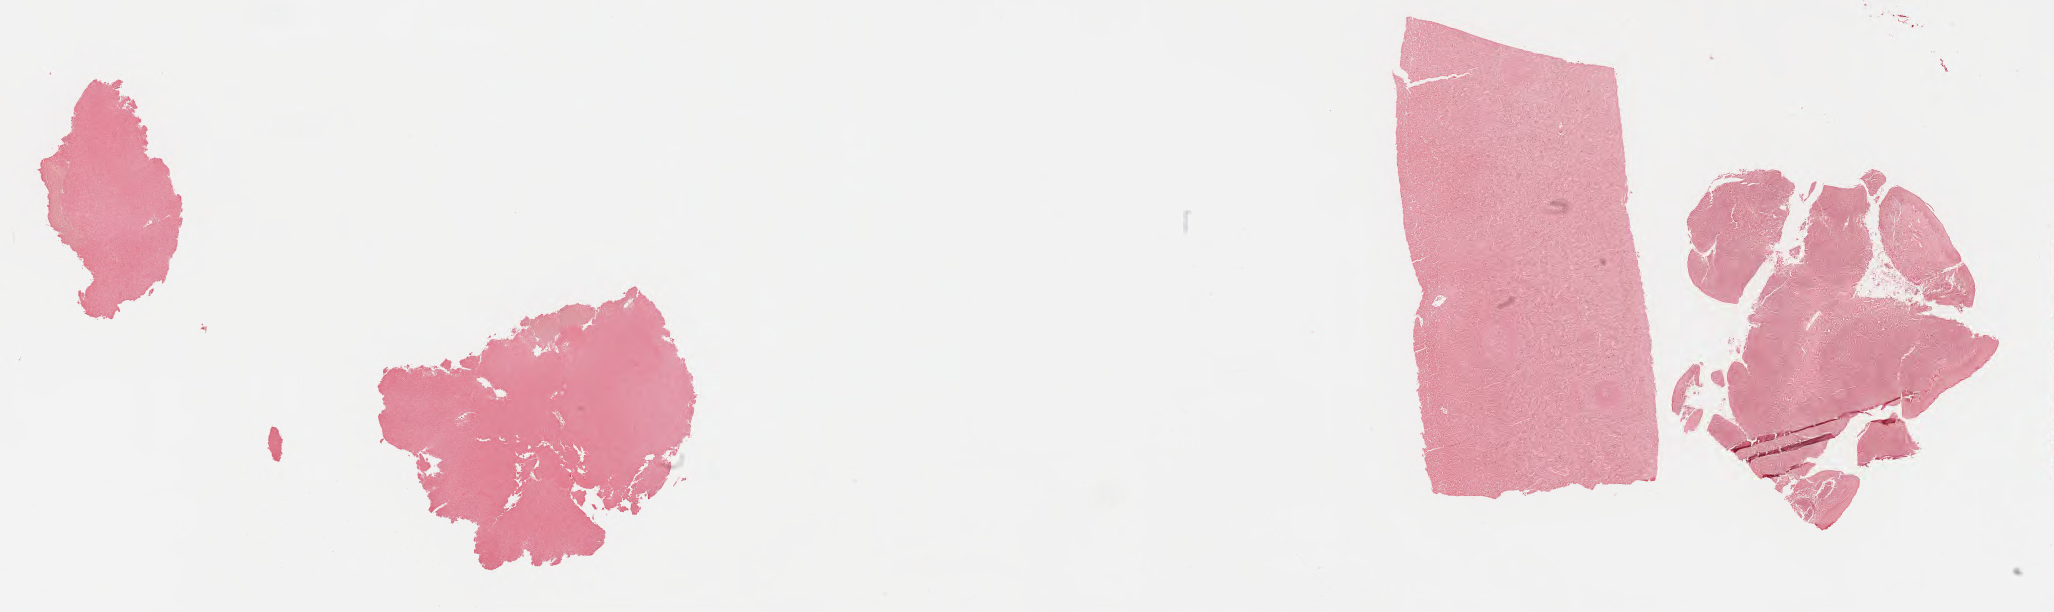
Whole-slide image, Epstein–Barr virus-encoded RNA (EBER) in-situ hybridisation, a low-resolution overview of the entire scanned area, about 33.2 x 9.9 mm; specimen: tumor tissue; site: lymph node. Patient: female, age 51 years.
Diagnosis: Diffuse large B-cell lymphoma, NOS.